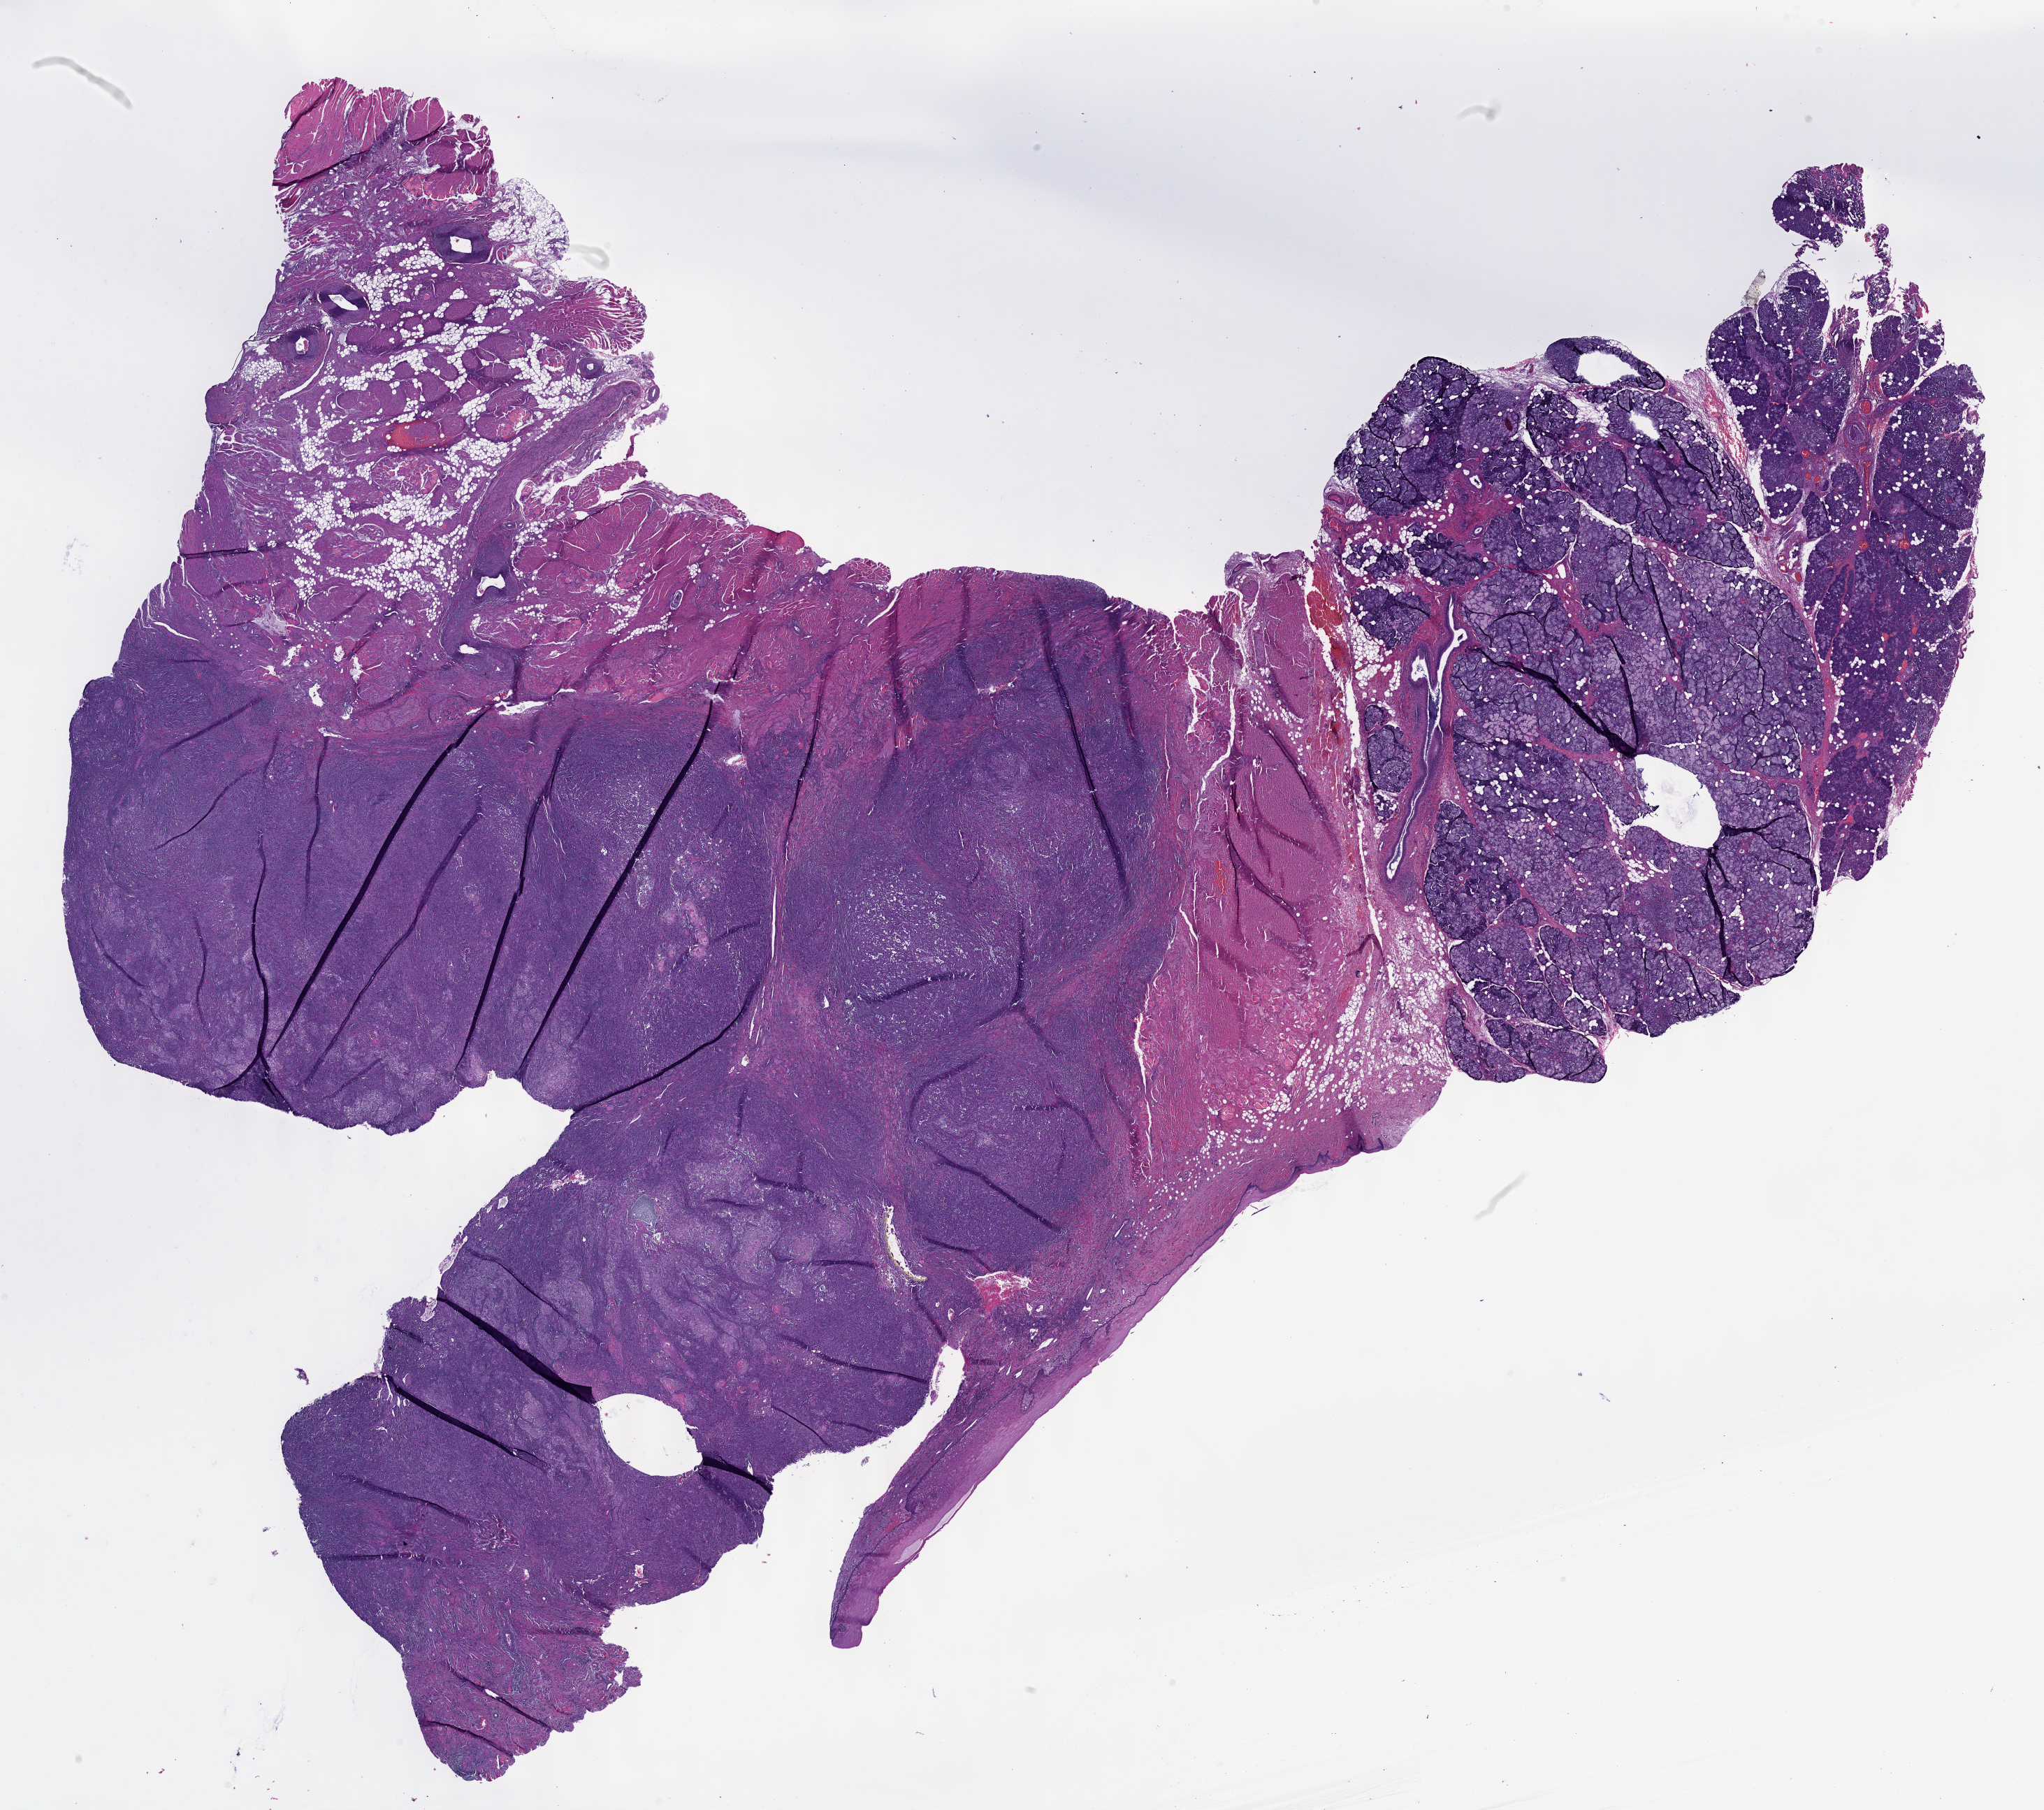
Digitized H&E-stained tissue section (whole slide) — shown as a low-resolution overview of the whole scanned area (about 23.6 x 20.9 mm); FFPE section; primary tumour sample from the head and neck. Patient: male, age at initial diagnosis 26 years. Histologic grade: G2 (moderately differentiated).
Lymph nodes positive (case pathology): 2 of 55 examined. Histologic diagnosis: Squamous cell carcinoma, NOS (tongue, NOS). TNM: T2 N2b. AJCC pathologic stage: IVA (7th edition).